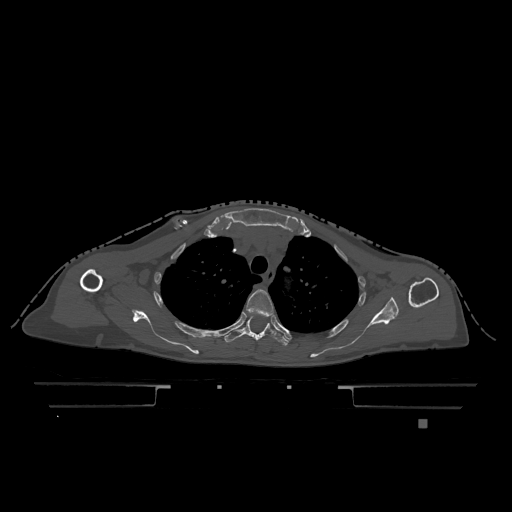
CT including the spine, one axial slice; bone window (W 1800 / L 400 HU); 0.5 mm slice thickness; 512 × 512 image matrix, field of view 500 × 500 mm. Female patient, age 74 years. Case-level facts recorded for this patient, not image findings: primary cancer: lung; vertebrae with lytic lesions (as recorded): T1, T4, T5, T6, L4, L5.
Outlined on this slice (semi-automatic segmentation, software-assisted and operator-edited):
- T3 vertebra: bounding box (x1, y1, x2, y2) in pixels: (246, 289, 274, 316)
- T4 vertebra: (224, 315, 292, 346)